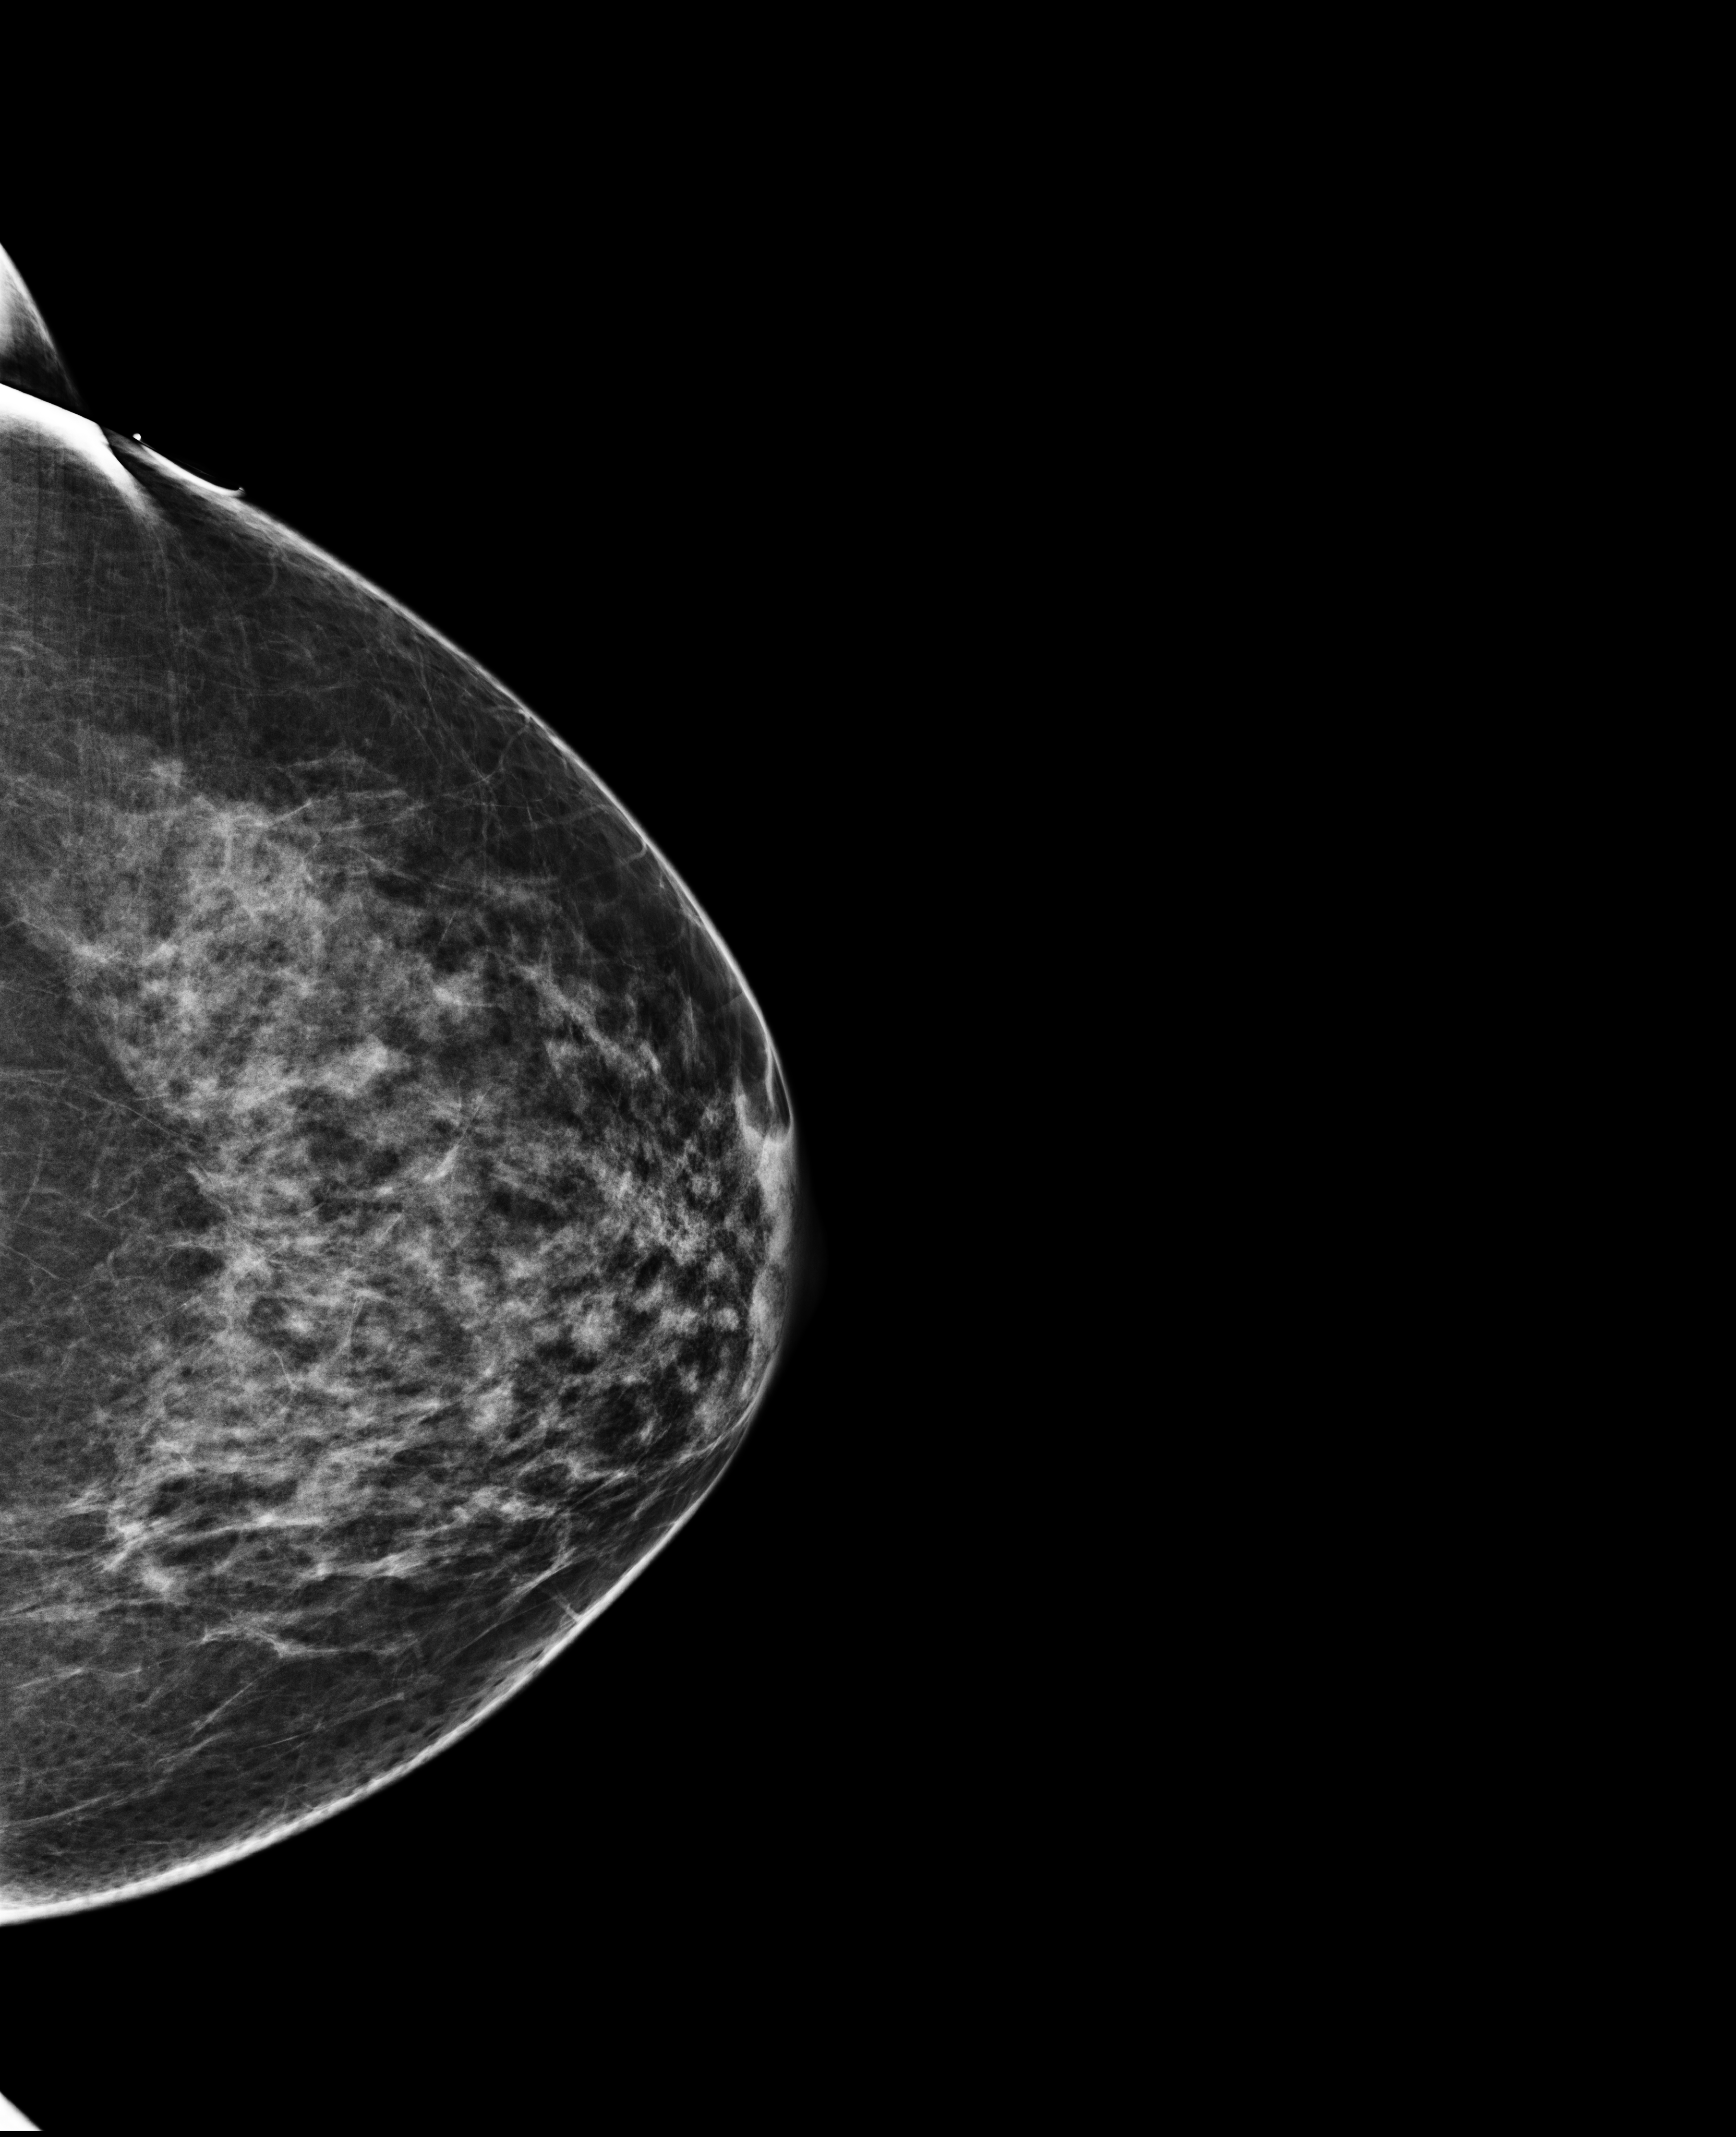
Screening examination, compressed breast thickness 70 mm, system: Selenia Dimensions. Patient aged 52 years (female).
Image type: full-field digital mammogram. Breast: left. Projection: CC view.